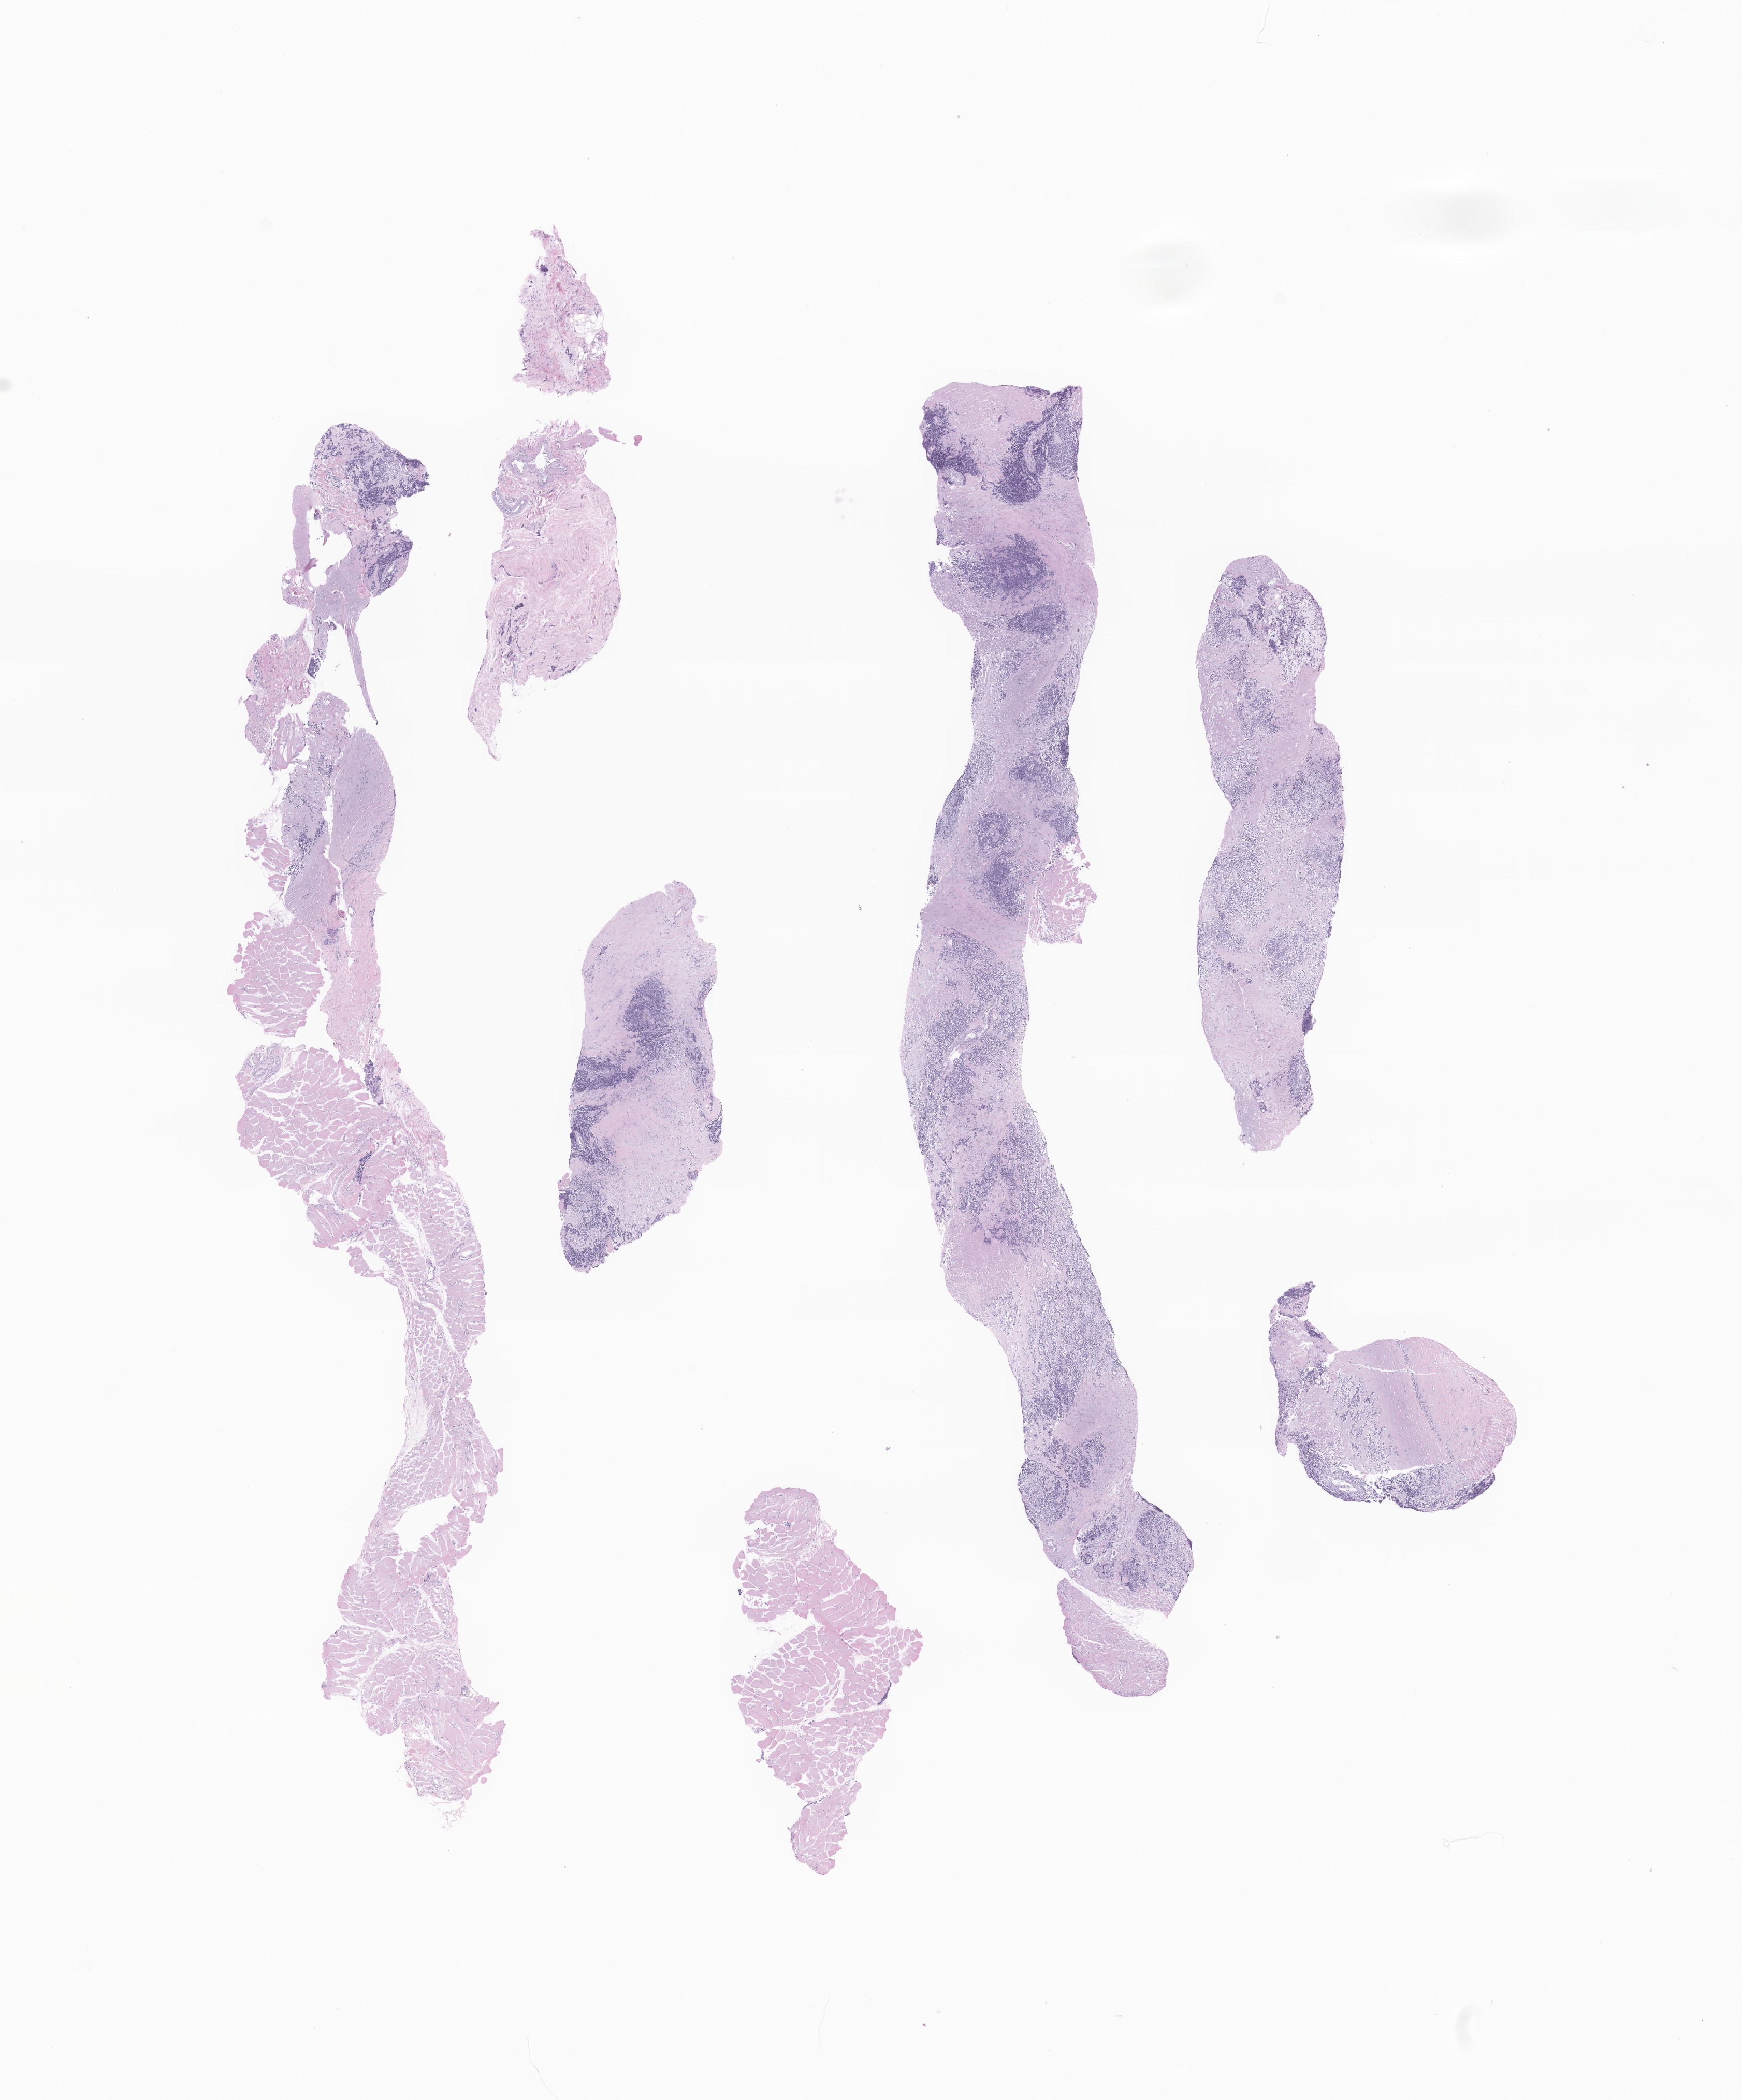
Digitized H&E-stained section of tumor tissue from the soft tissue of lower extremity, a low-resolution overview of the entire scanned area, about 14.2 x 17.1 mm. Formalin-fixed paraffin-embedded section. Patient: male, age 154 months (12 years 10 months).
- diagnosis: Rhabdomyosarcoma, NOS